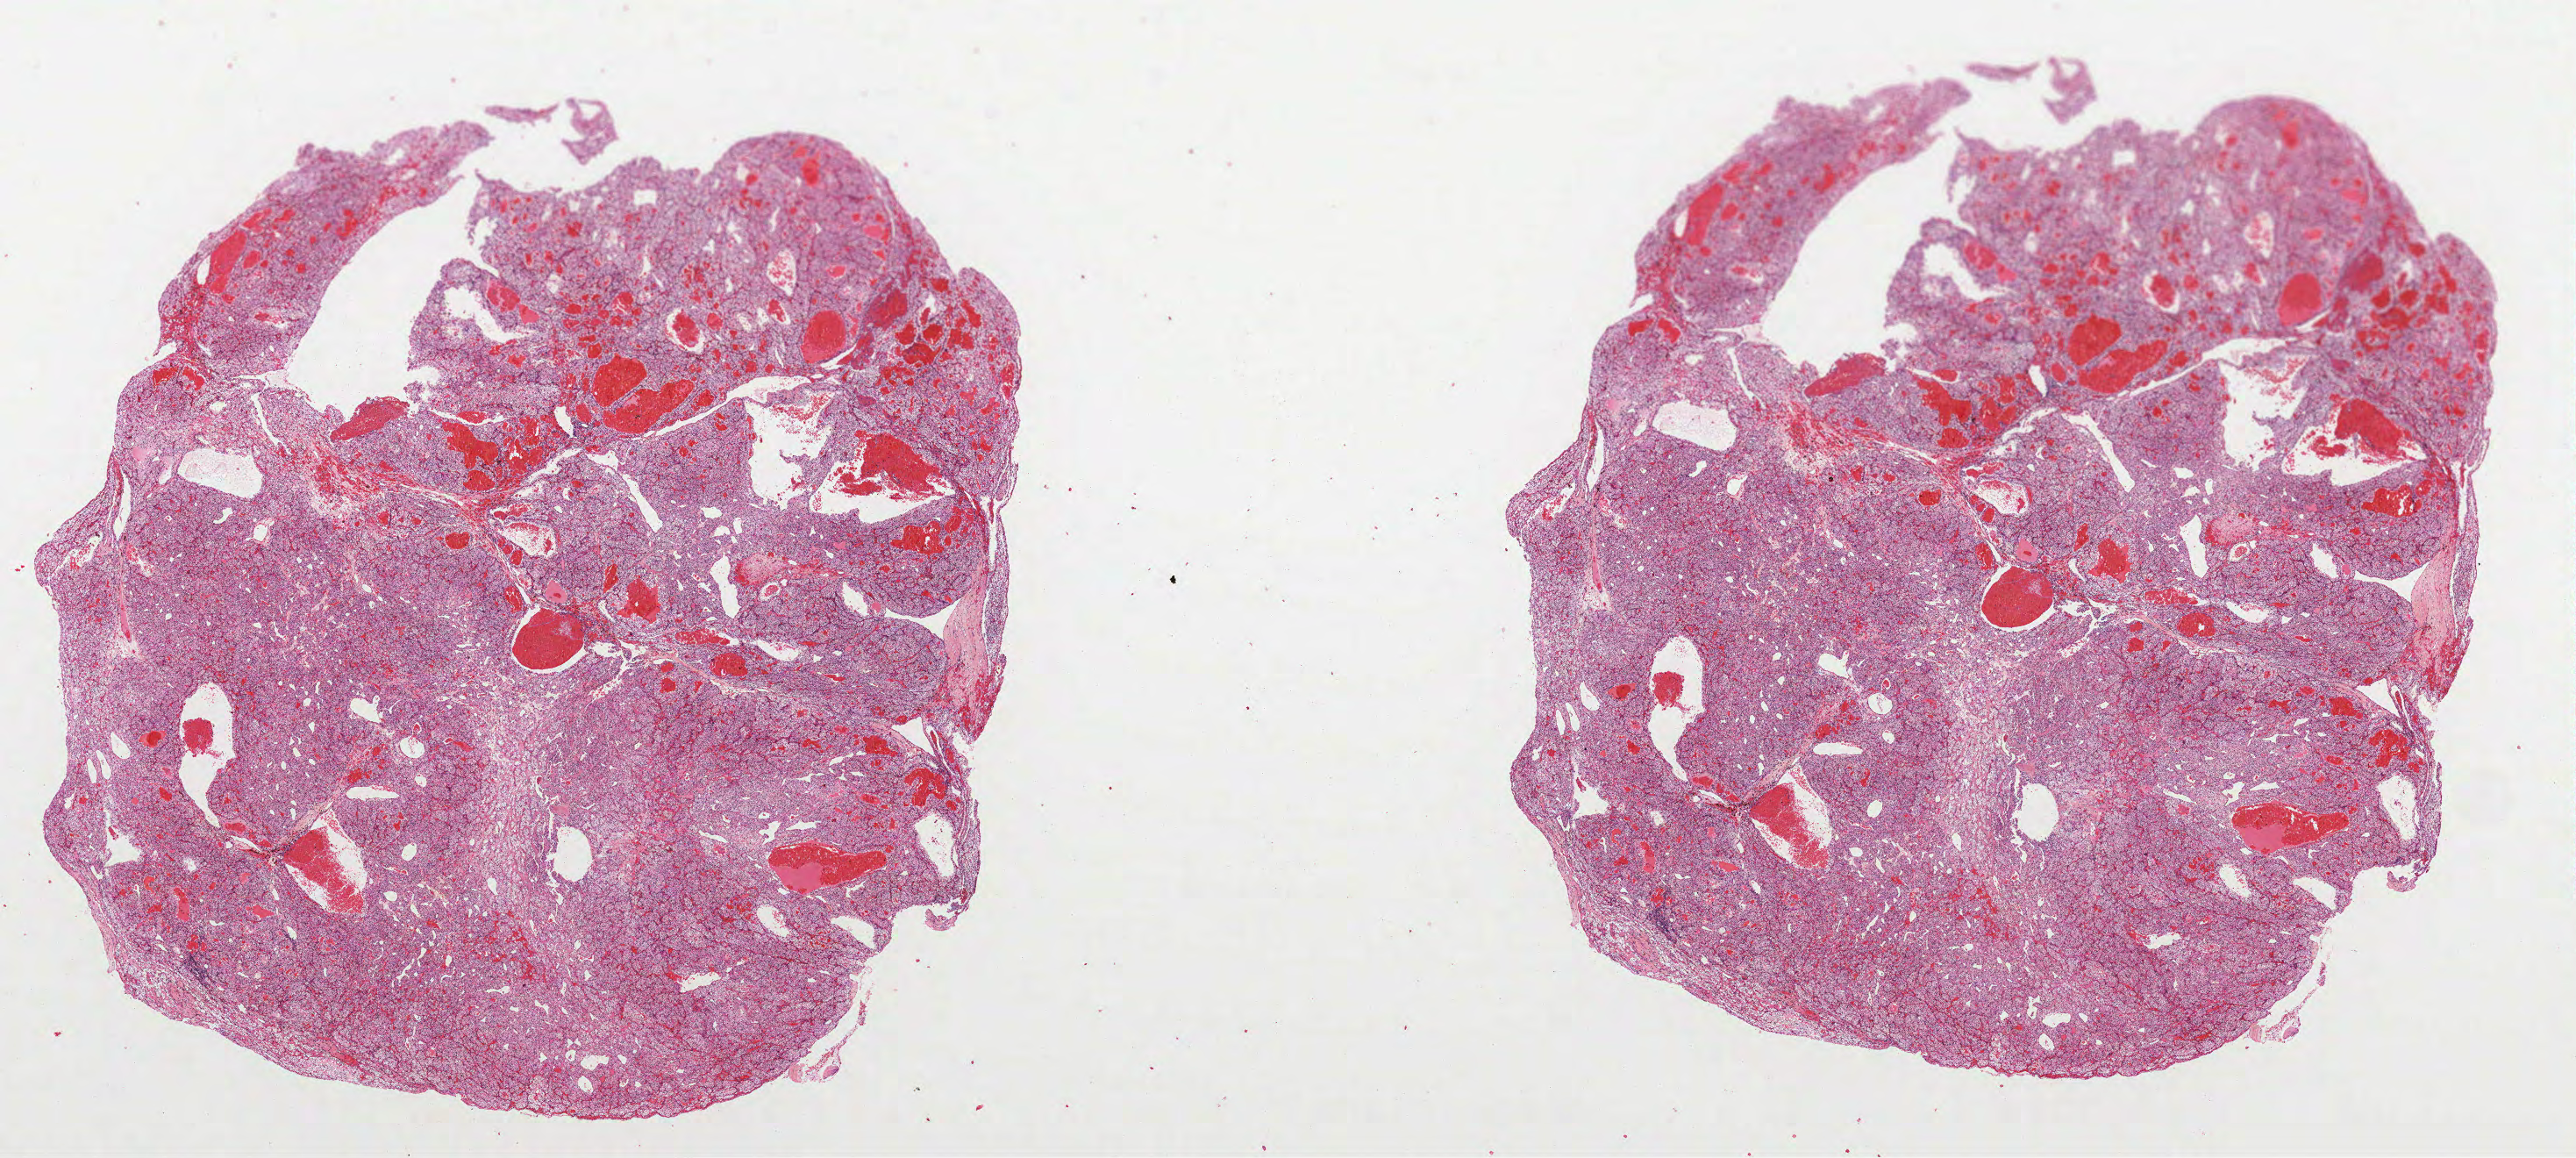
Digitized H&E-stained tissue section (whole slide) — a low-resolution overview of the entire scanned area, about 23.7 x 10.6 mm (acquisition: 40x scan); formalin-fixed paraffin-embedded (FFPE) diagnostic section; primary tumour sample from the kidney. Female patient; age at initial diagnosis 41 years. Histologic grade: G2 (moderately differentiated).
TNM: T1b NX M0. Pathologic diagnosis: Clear cell adenocarcinoma, NOS. Laterality: right. AJCC pathologic stage: I (6th edition).